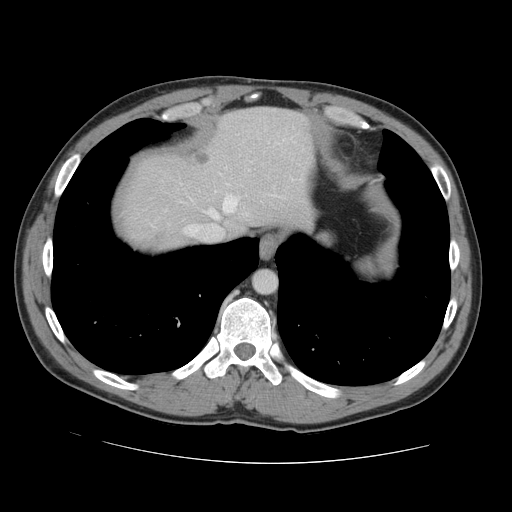
Contrast-enhanced abdominal CT, one axial slice. Position 122 of 131 along the scan axis. 120 kVp. Intravenous contrast given. Soft-tissue window (W 400 / L 40 HU). 2.5 mm slice thickness. 512 × 512 image matrix. Male patient, age 40 years. Case-level facts recorded for this patient, not image findings: diagnosis: colorectal cancer liver metastases, imaged before liver resection; multiple liver metastases: yes; largest metastasis: 2.9 cm.
Structures marked on this image (expert manual segmentation):
- hepatic veins: bounding box <186,197,237,235> (left, top, right, bottom; pixels)
- liver: <127,108,310,250>
- planned liver remnant (the part of the liver to remain after resection): <135,108,311,235>
- liver metastasis: <194,154,209,162>